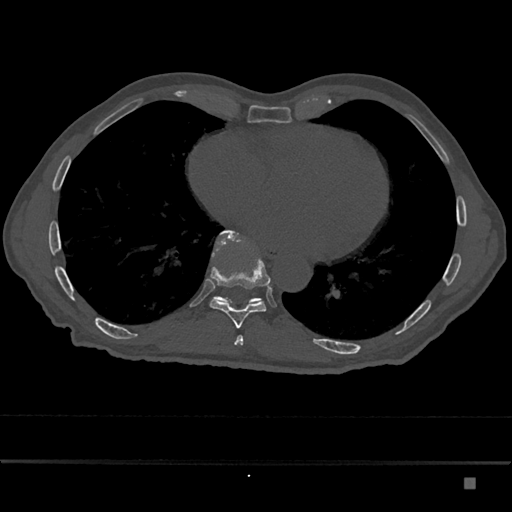
CT including the spine, one axial slice. Slice 790 of 797 in the series (ordered by position). Reconstruction kernel Br40s/3. Bone window (W 1800 / L 400 HU). 0.5 mm slice thickness. 512 × 512 image matrix, field of view 390 × 390 mm. Patient: male, 72 years. From the clinical record (not read from this slice): primary cancer: prostate.
Annotated regions visible in this slice (semi-automatic segmentation, software-assisted and operator-edited):
- T10 vertebra: bounding box [x1, y1, x2, y2] px = [212, 230, 264, 304]
- T9 vertebra: [209, 230, 271, 328]